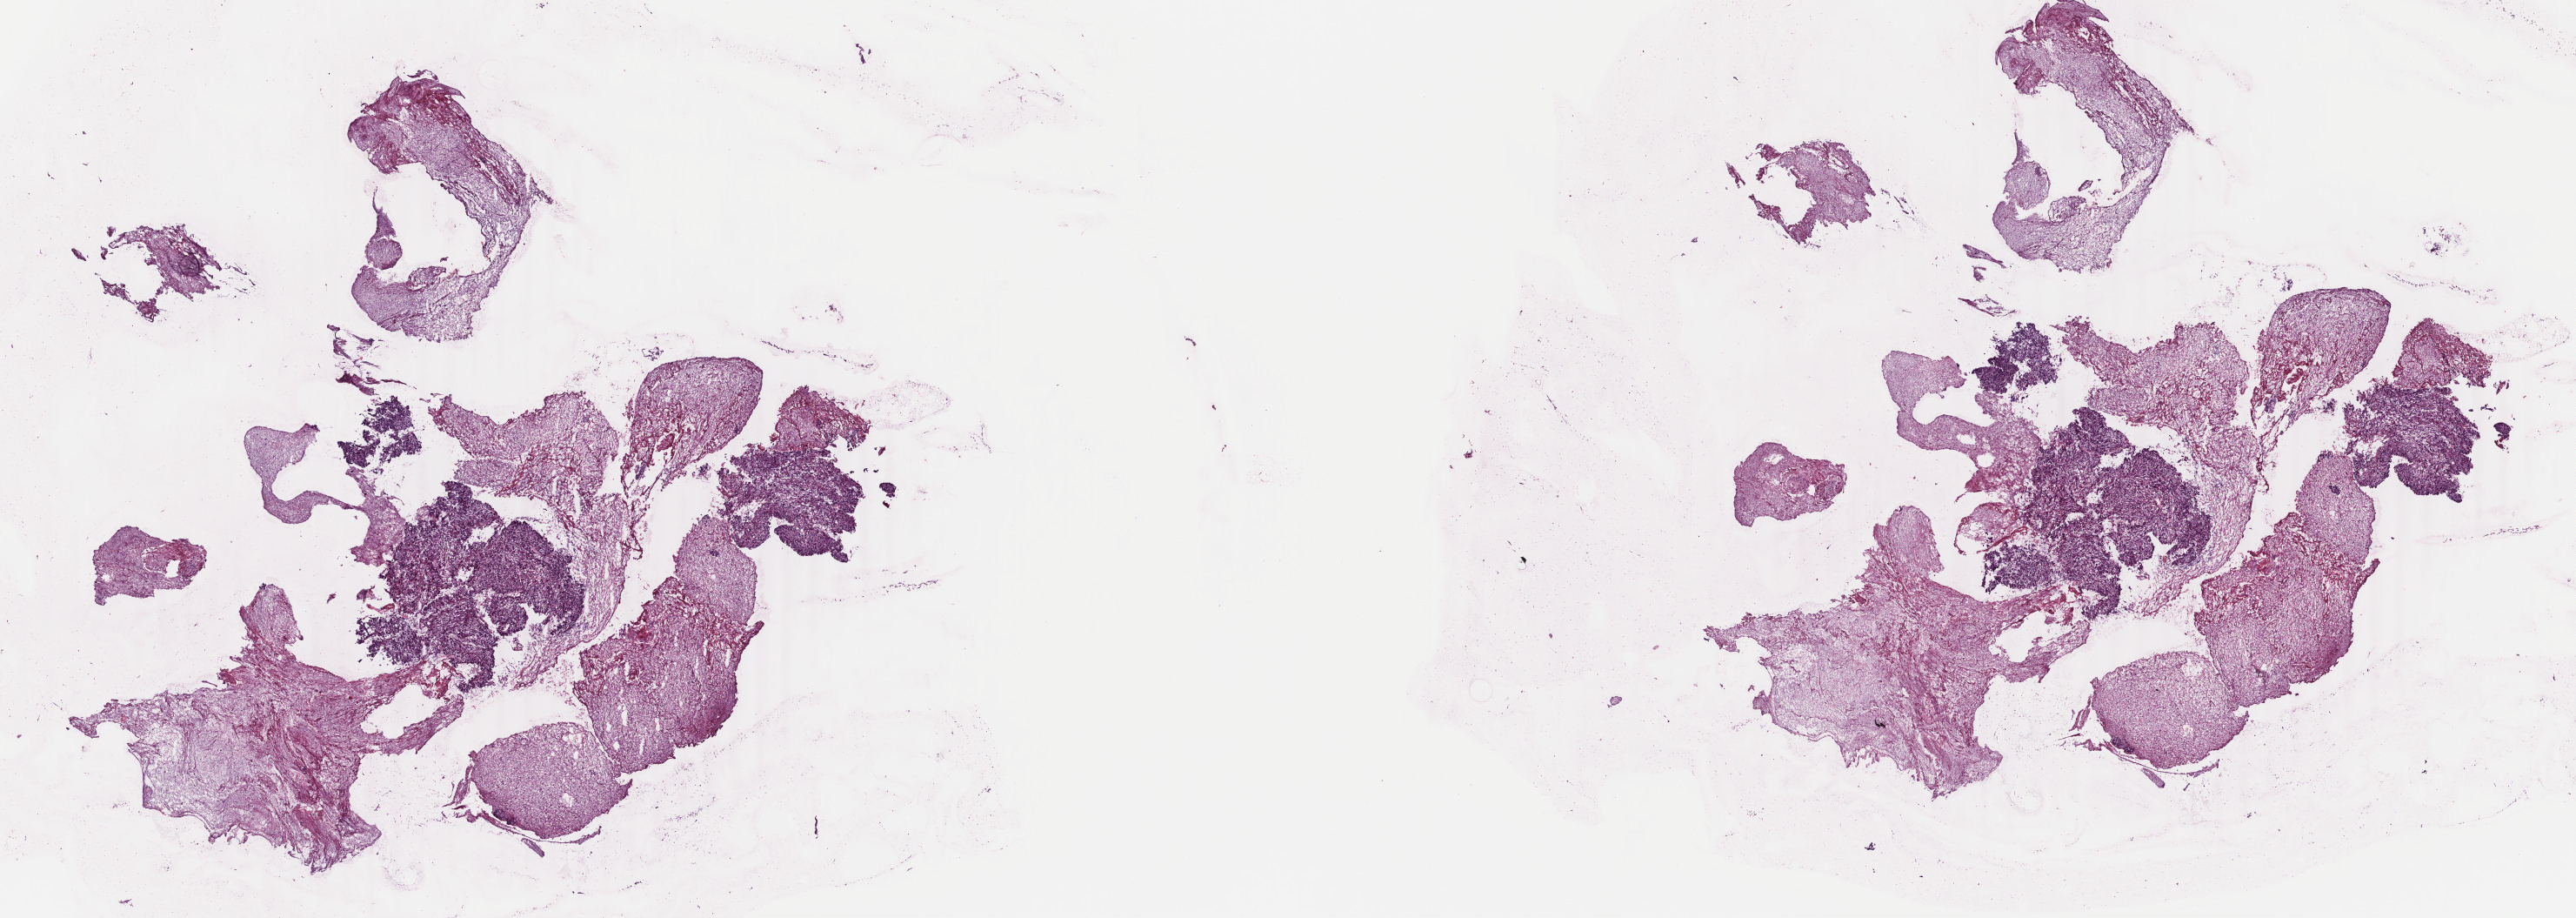
H&E-stained whole-slide image, low-resolution overview of the scanned area, about 23.6 x 8.4 mm. Frozen section. Primary tumour sample from the cervix. Female patient; age at initial diagnosis 64 years. Histologic grade: G2 (moderately differentiated). Composition of this section per pathologist review: tumour cells 30%, tumour nuclei 98%, normal cells 0%, stromal cells 65%, necrosis 5%. Inflammatory infiltration, as recorded: lymphocyte infiltration 1%, monocyte infiltration 0%, neutrophil infiltration 0%.
FIGO stage: IIIB. Lymph nodes positive (case pathology): 0 of 14 examined. Pathologic diagnosis: Squamous cell carcinoma, NOS (cervix uteri).